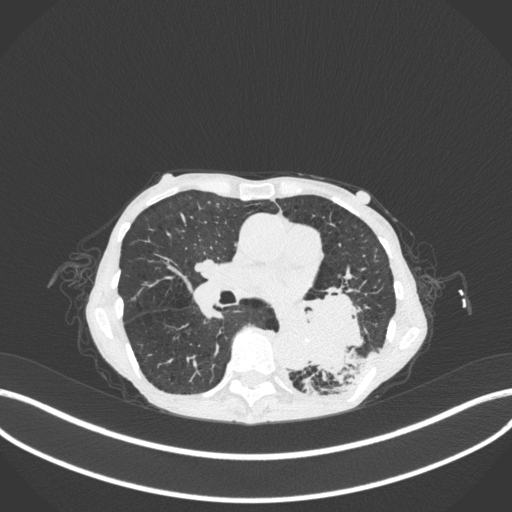
Chest CT, one axial slice. Slice 140 of 347 in the series (ordered by position). 120 kVp. Lung window (W 1500 / L -600 HU). 1 mm slice thickness. 512 × 512 image matrix. Female patient, age 70 years. Case-level facts recorded for this patient, not image findings: clinical TNM (as recorded): T3 N0 M0.
Structures marked on this image (bounding box drawn by a radiologist):
- lung tumour (recorded histology: small cell carcinoma): box from (x=293, y=286) to (x=367, y=374) px